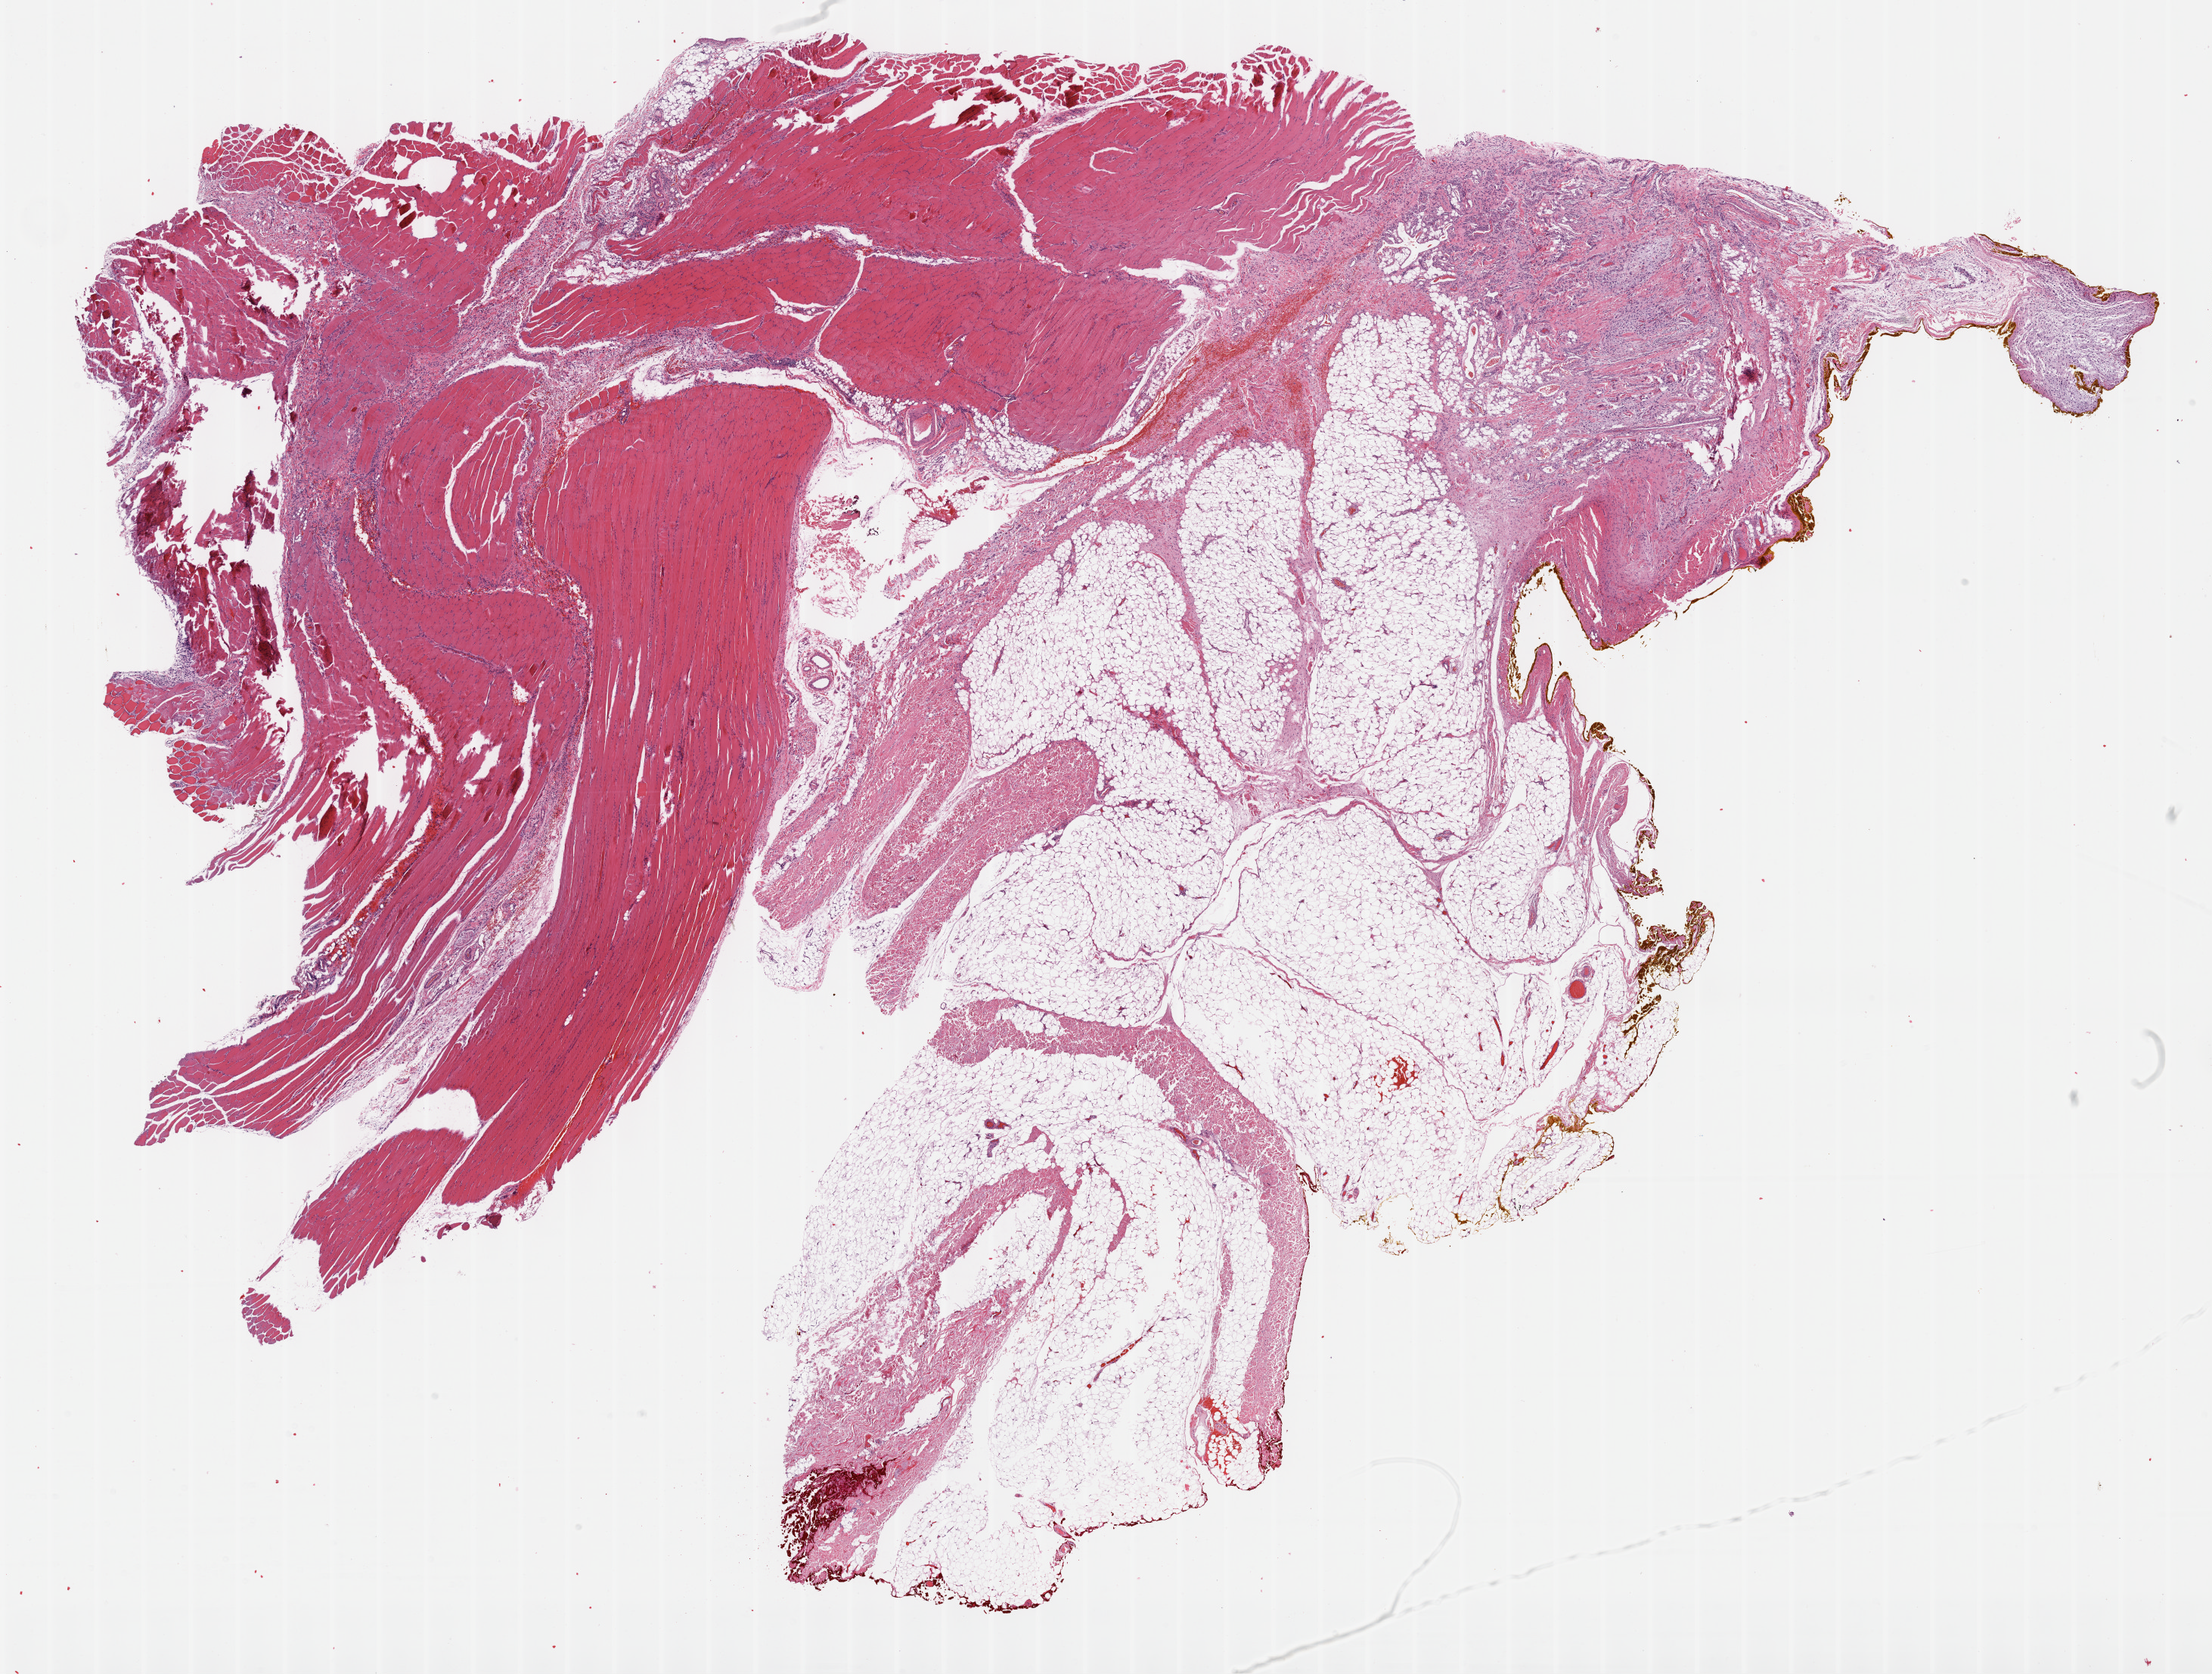
Digitized Hematoxylin and eosin (H&E) stained tissue section (whole slide) — whole scanned area (about 23.7 x 17.9 mm, from a 40x scan) shown as a low-resolution overview, formalin-fixed paraffin-embedded (FFPE) diagnostic section, connective, subcutaneous and other soft tissues, primary tumour sample. Patient: male, age at initial diagnosis 35 years.
Diagnosis: Fibromyxosarcoma.